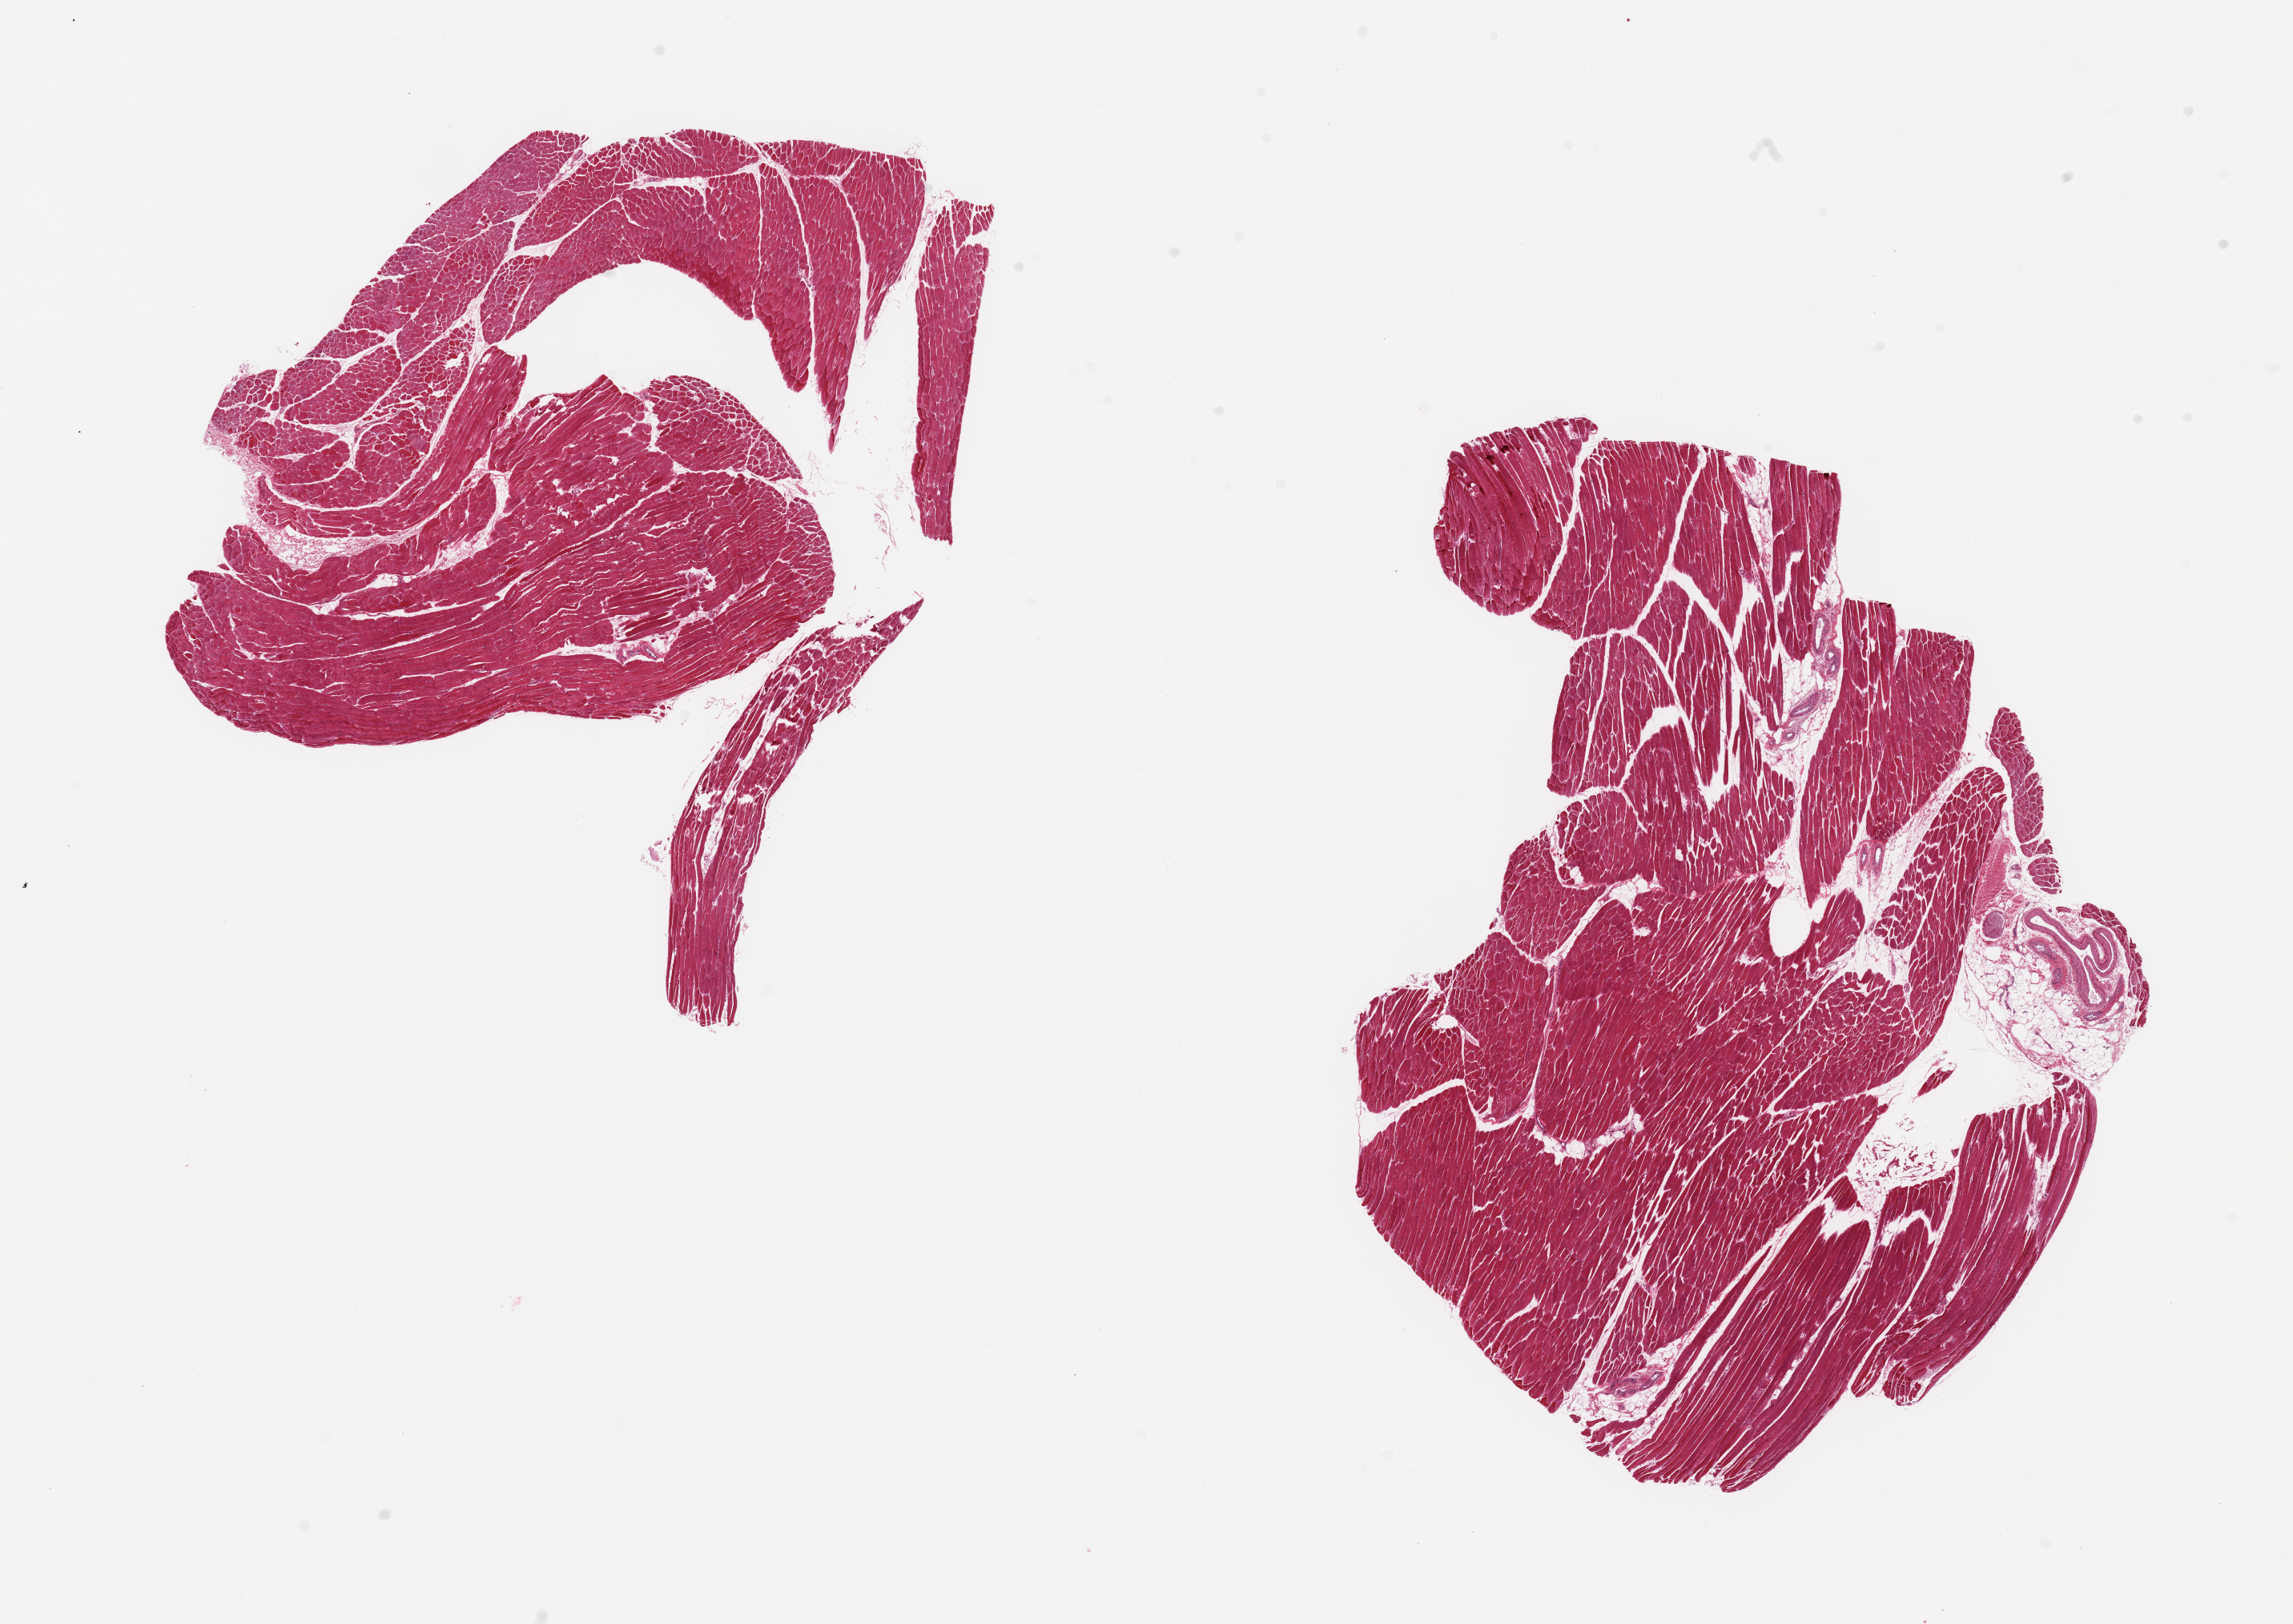
Whole-slide image, hematoxylin and eosin (H&E) stain, brightfield — low-resolution overview of the scanned area, about 22.6 x 16.0 mm. PAXgene-fixed paraffin-embedded (PFPE) section. Section of skeletal muscle (target tissue). Tissue donor sample. Donor sex: male.
Pathologist's review note for this sample: 2 pieces, ~10% interstitial fat.